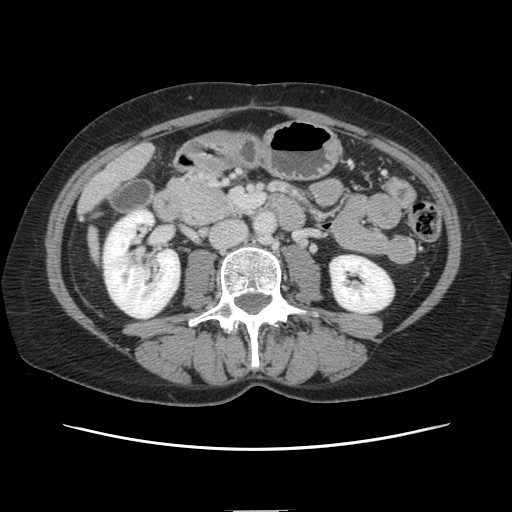
Contrast-enhanced abdominal CT, one axial slice. Position 33 of 141 along the scan axis. 120 kVp. Intravenous contrast given. Soft-tissue window (W 400 / L 40 HU). 512 × 512 image matrix, field of view 350 × 350 mm. Female patient, age 63 years. Case-level facts recorded for this patient, not image findings: diagnosis: colorectal cancer liver metastases, imaged before liver resection; multiple liver metastases: yes; largest metastasis: 3.2 cm.
Structures marked on this image (outlined manually by an expert reader):
- liver: bounding box <82,145,153,210> (left, top, right, bottom; pixels)